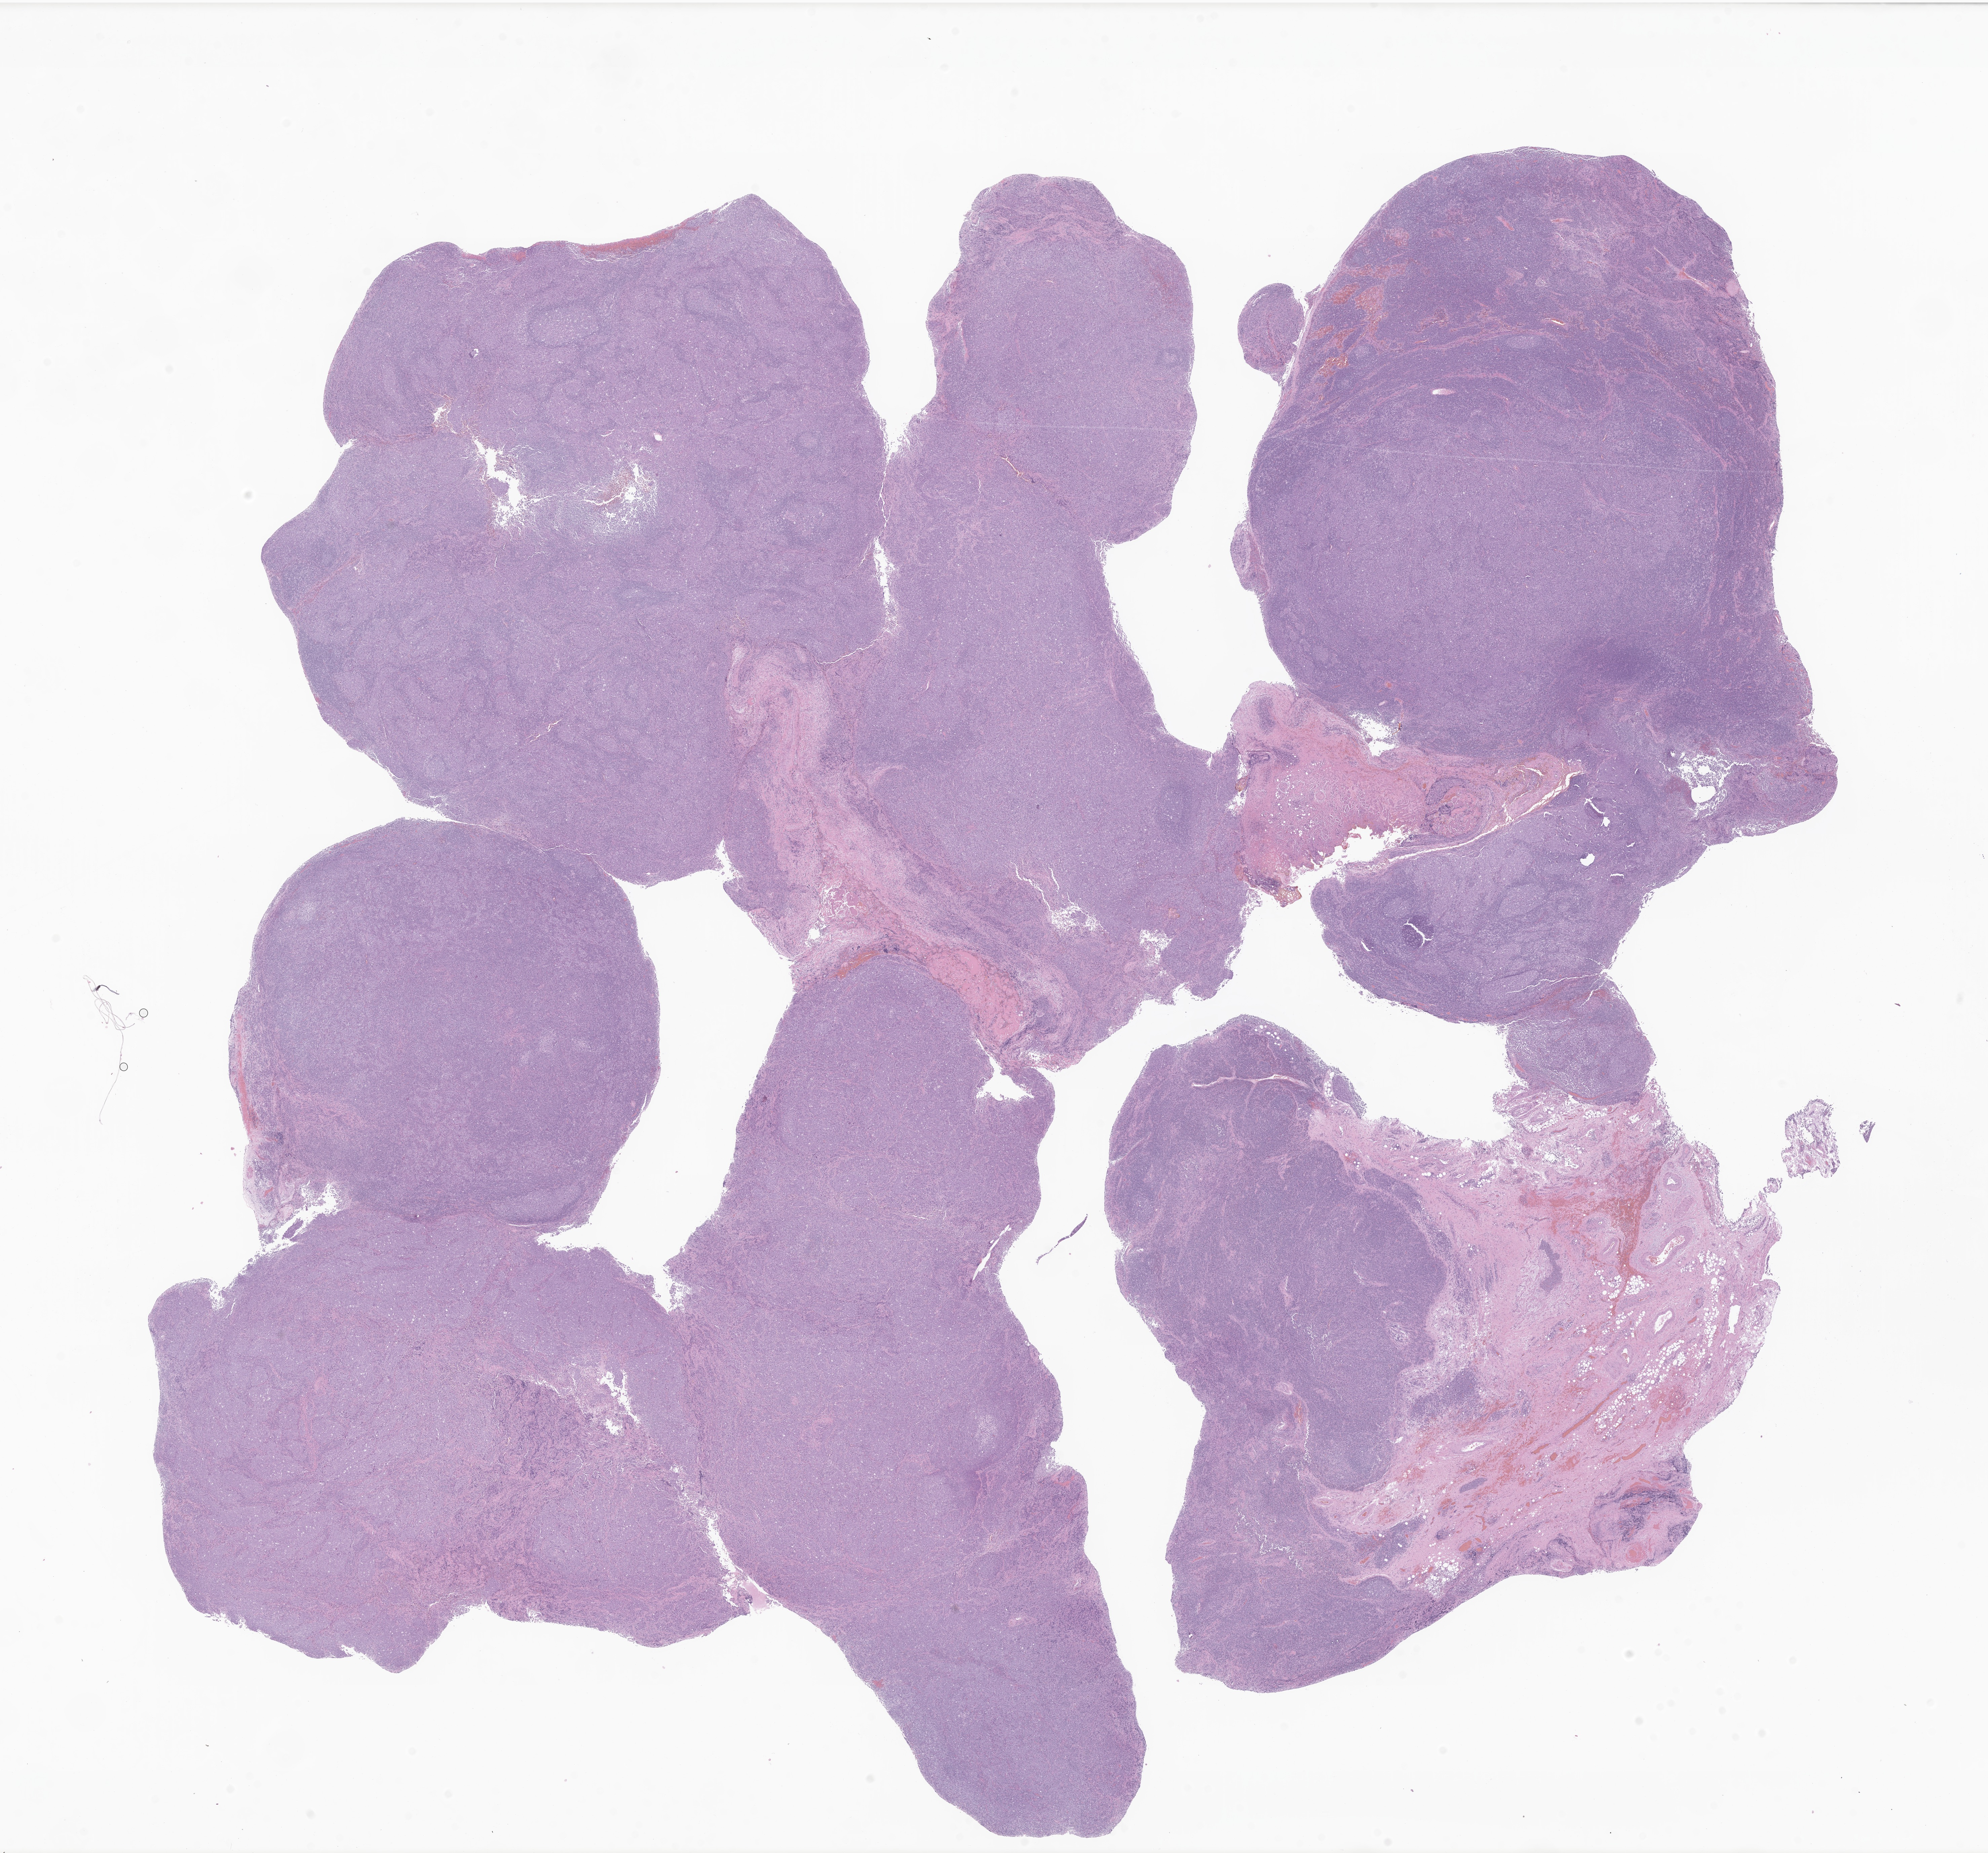
Hematoxylin and eosin (H&E) whole-slide image of tumor tissue from the nasopharynx — low-resolution overview of the scanned area, about 24.9 x 23.2 mm, formalin-fixed paraffin-embedded section. Male patient, age 221 months (18 years 5 months).
Diagnosis: Squamous cell carcinoma, large cell, nonkeratinizing, NOS.